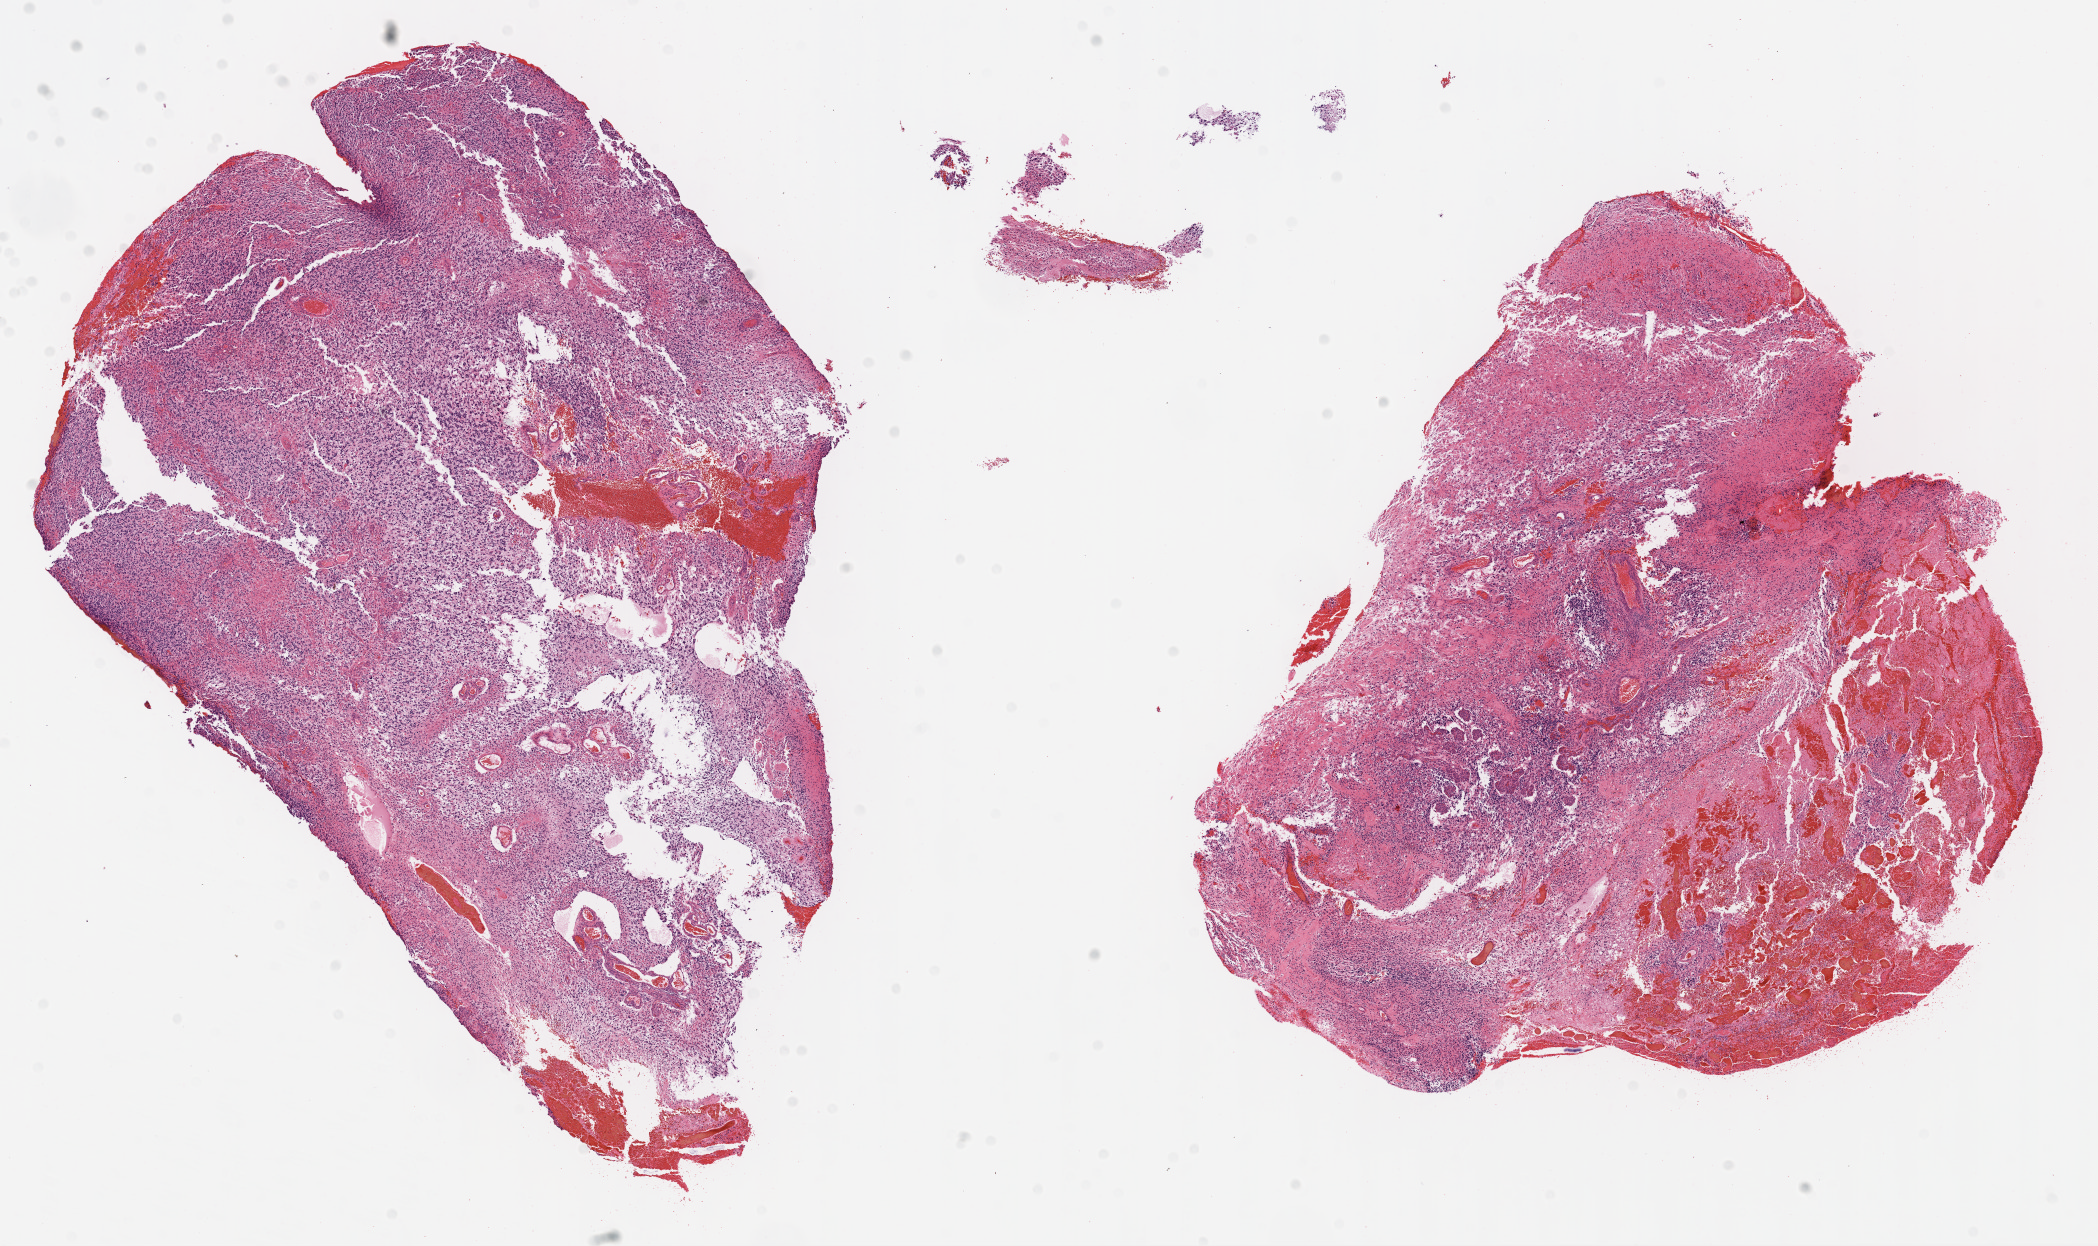
H&E-stained whole-slide image, whole scanned area (about 16.9 x 10.1 mm) shown as a low-resolution overview. Formalin-fixed paraffin-embedded (FFPE) diagnostic section. Sample: primary tumour, brain. Male, age 31 years at initial diagnosis.
Diagnosis: Glioblastoma.